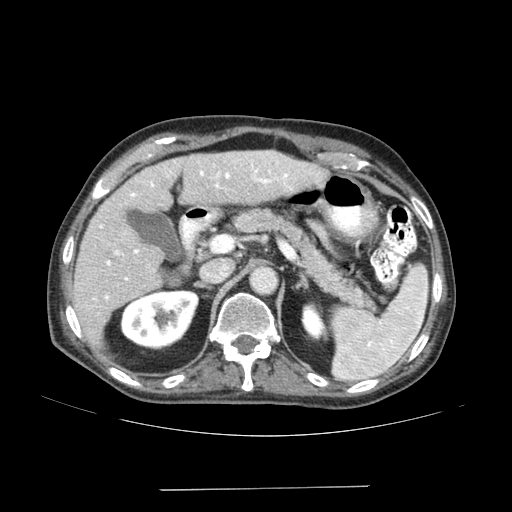
Contrast-enhanced abdominal CT (liver protocol), one axial slice; slice 94 of 192 in the series (ordered by position); soft-tissue window (W 400 / L 40 HU); 2.5 mm slice thickness; 512 × 512 image matrix. Case-level facts recorded for this patient, not image findings: diagnosis: hepatocellular carcinoma (patient treated with transarterial chemoembolisation; whether this scan precedes or follows treatment is not stated here); TNM stage (as recorded): Stage-IVA; Child-Pugh class: A; tumour differentiation: poorly differentiated; tumour nodularity: uninodular.
Structures marked on this image (semi-automatic segmentation, software-assisted and operator-edited):
- liver parenchyma outside the tumour (the mass and vessels are separate outlines, so this box may not span the whole liver): bounding box (x1, y1, x2, y2) in pixels: (70, 150, 326, 346)
- liver vessels: (100, 161, 291, 299)